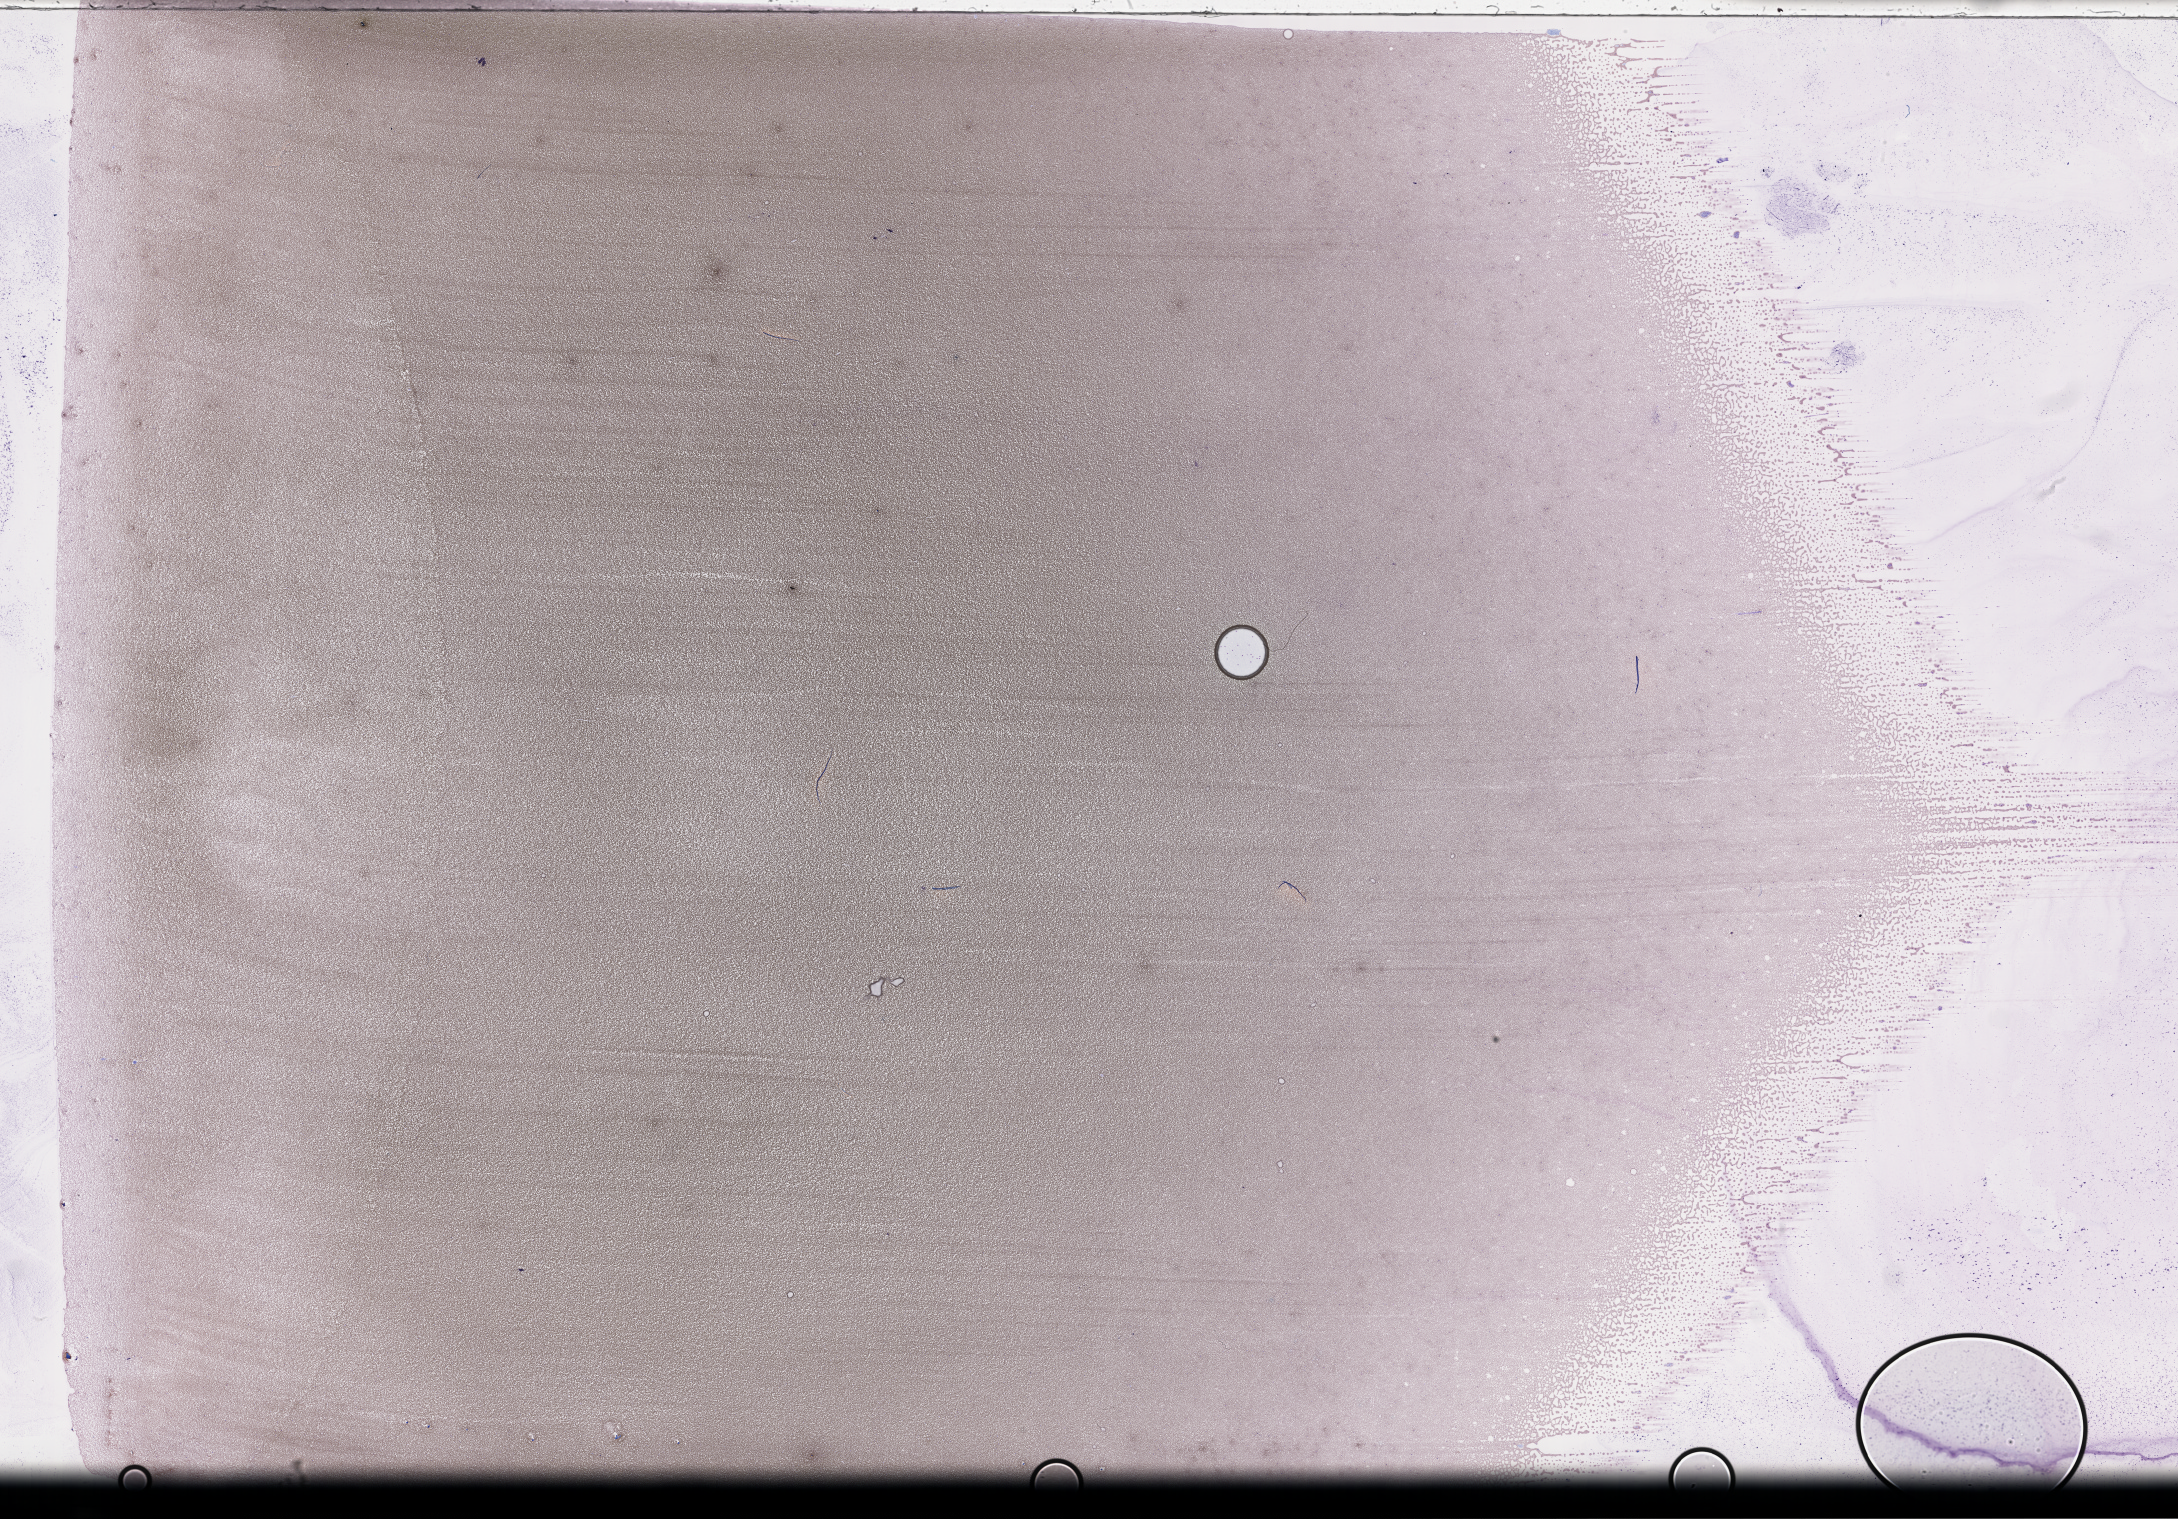
Wright-Giemsa-stained whole blood smear, whole-slide image, whole scanned area (about 35.2 x 24.5 mm) shown as a low-resolution overview, EDTA-anticoagulated smear, collected on treatment. Female patient.
• from a patient with: Plasma Cell Myeloma